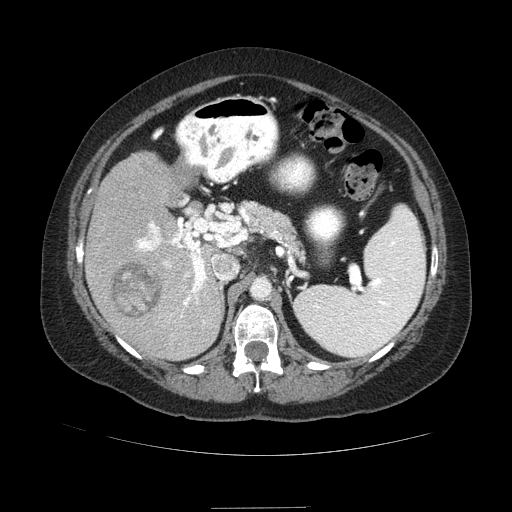
Contrast-enhanced abdominal CT (liver protocol), one axial slice. Position 49 of 89 along the scan axis. Reconstruction kernel STANDARD. 120 kVp. Soft-tissue window (W 400 / L 40 HU). 2.5 mm slice thickness. 512 × 512 image matrix, field of view 400 × 400 mm. Case-level facts recorded for this patient, not image findings: diagnosis: hepatocellular carcinoma (patient treated with transarterial chemoembolisation; whether this scan precedes or follows treatment is not stated here); TNM stage (as recorded): Stage-IIIB; Child-Pugh class: A.
Outlined on this slice (semi-automatically segmented with operator editing):
- liver parenchyma outside the tumour (the mass and vessels are separate outlines, so this box may not span the whole liver): bounding box [x1, y1, x2, y2] px = [86, 151, 234, 360]
- mass: [109, 260, 160, 318]
- liver vessels: [136, 222, 225, 324]